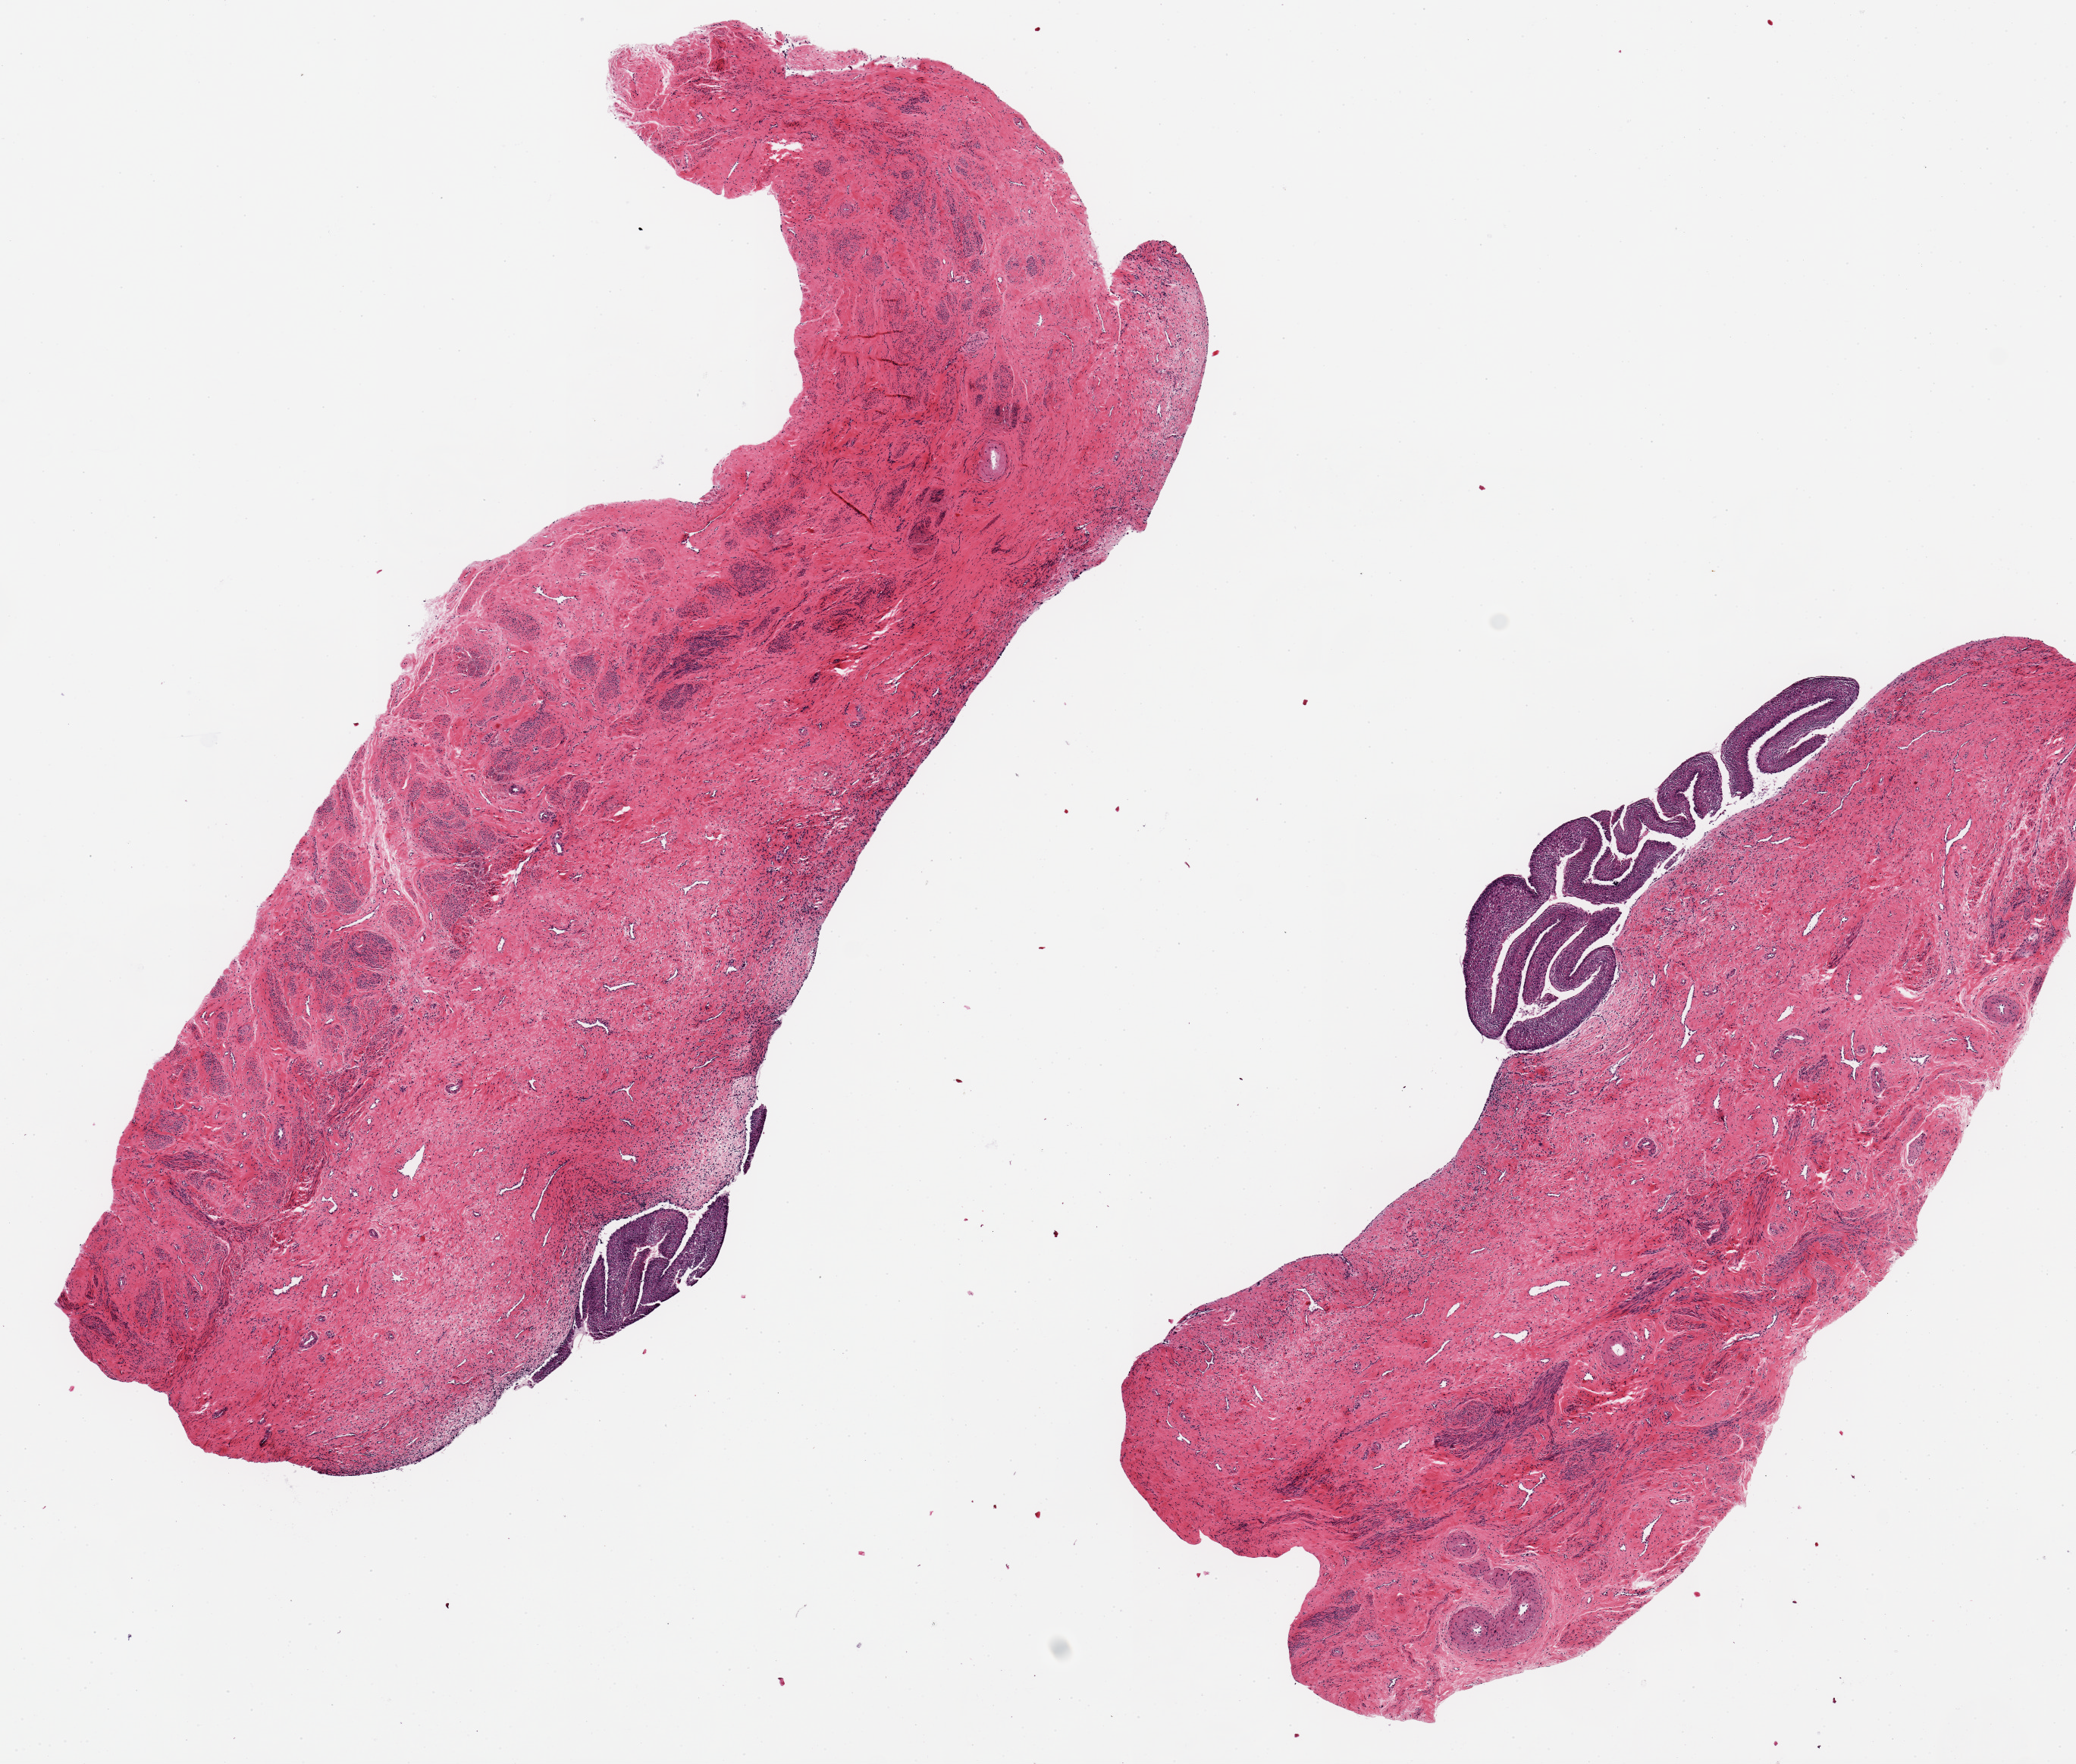
Whole-slide image, hematoxylin and eosin (H&E) stain — low-resolution overview of the scanned area, about 10.8 x 9.2 mm. PAXgene-fixed paraffin-embedded (PFPE) section. Sampled site (target tissue): exocervix. Tissue donor sample. Female donor.
- review note (as recorded): 2 pieces ~8x2.6mm; epithelium folded